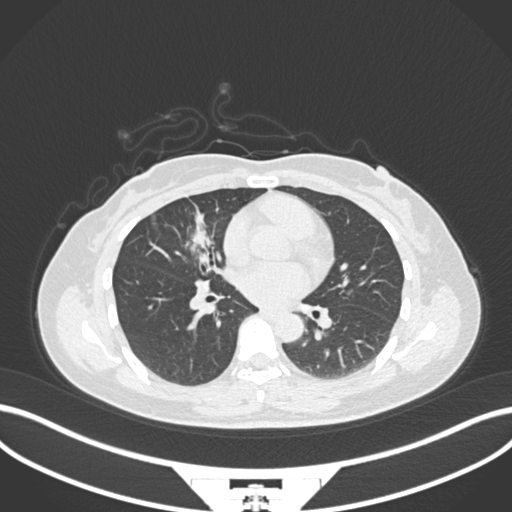
Chest CT, one axial slice. Position 81 of 171 along the scan axis. Lung window (W 1500 / L -600 HU). 512 × 512 image matrix, field of view 400 × 400 mm. Patient: female, 43 years. Case-level facts recorded for this patient, not image findings: clinical TNM (as recorded): T1c N3 M1; histopathological grade: G1.
Structures marked on this image (rectangle marked by the reading radiologist):
- lung tumour (recorded histology: adenocarcinoma): bounding box [x1, y1, x2, y2] px = [182, 213, 219, 258]